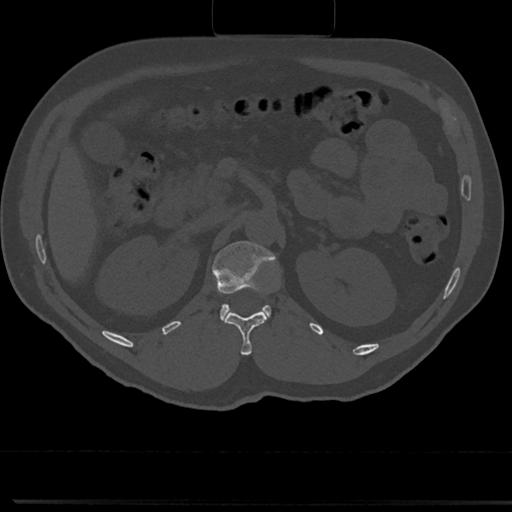
CT including the spine, one axial slice. Position 113 of 817 along the scan axis. Reconstruction kernel Br40s/3. 120 kVp. Bone window (W 1800 / L 400 HU). 0.5 mm slice thickness. 512 × 512 image matrix, field of view 355 × 355 mm. Patient: male, 61 years. From the clinical record (not read from this slice): primary cancer: prostate.
Structures marked on this image (semi-automatically segmented with operator editing):
- L1 vertebra: bounding box <212,240,278,326> (left, top, right, bottom; pixels)
- T12 vertebra: <223,311,268,355>